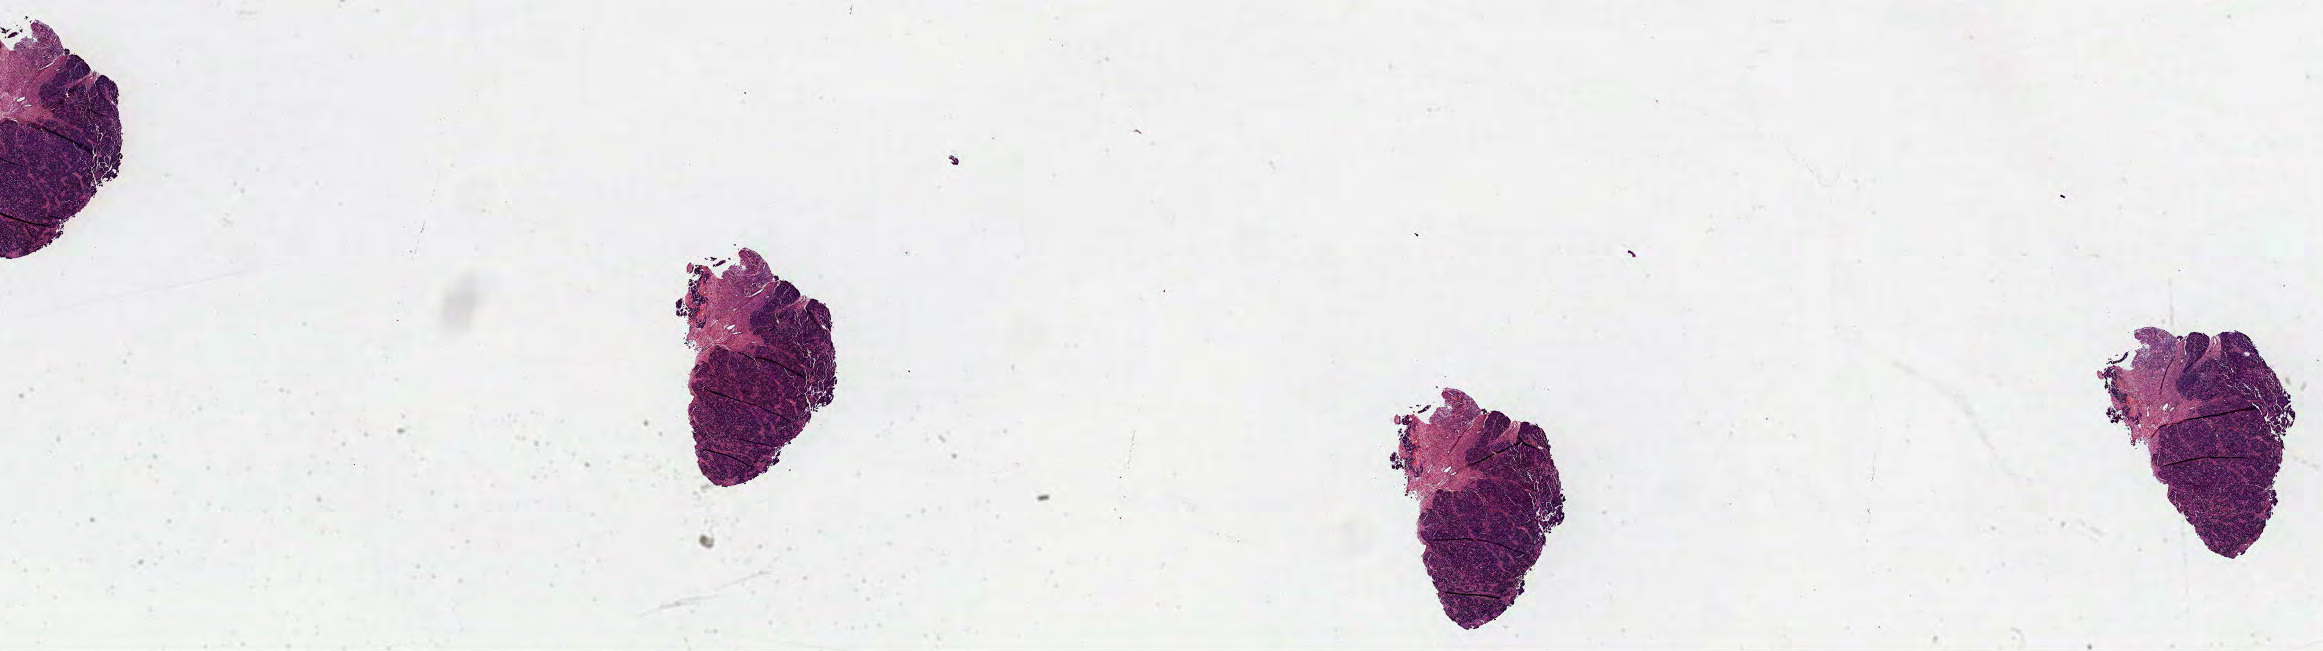
Digitized H&E tissue section (whole slide), a low-resolution overview of the entire scanned area, about 37.5 x 10.5 mm (acquisition: 40x scan); formalin-fixed paraffin-embedded (FFPE) diagnostic section; primary tumour sample from the ovary. Female patient; age at initial diagnosis 67 years. Histologic grade: G3 (poorly differentiated).
- FIGO stage: IIIC
- laterality: bilateral
- diagnosis: Serous cystadenocarcinoma, NOS